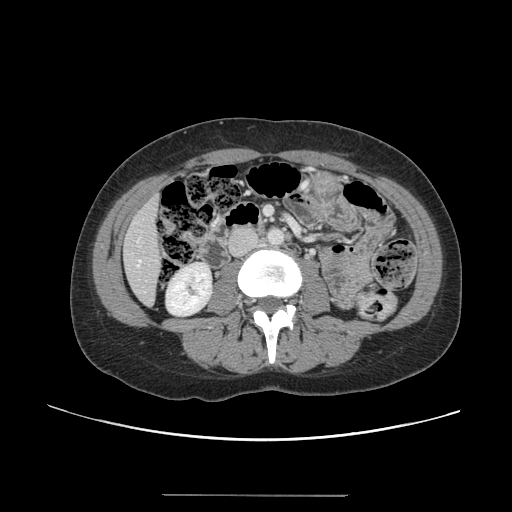
Contrast-enhanced abdominal CT, one axial slice; position 33 of 144 along the scan axis; 120 kVp; soft-tissue window (W 400 / L 40 HU); 512 × 512 image matrix, field of view 380 × 380 mm. Female patient, age 53 years. Case-level facts recorded for this patient, not image findings: diagnosis: colorectal cancer liver metastases, imaged before liver resection; multiple liver metastases: yes; largest metastasis: 1.1 cm.
Structures marked on this image (expert manual segmentation):
- hepatic veins: bounding box (x1, y1, x2, y2) in pixels: (138, 260, 141, 266)
- liver: (124, 200, 163, 303)
- planned liver remnant (the part of the liver to remain after resection): (124, 198, 163, 304)